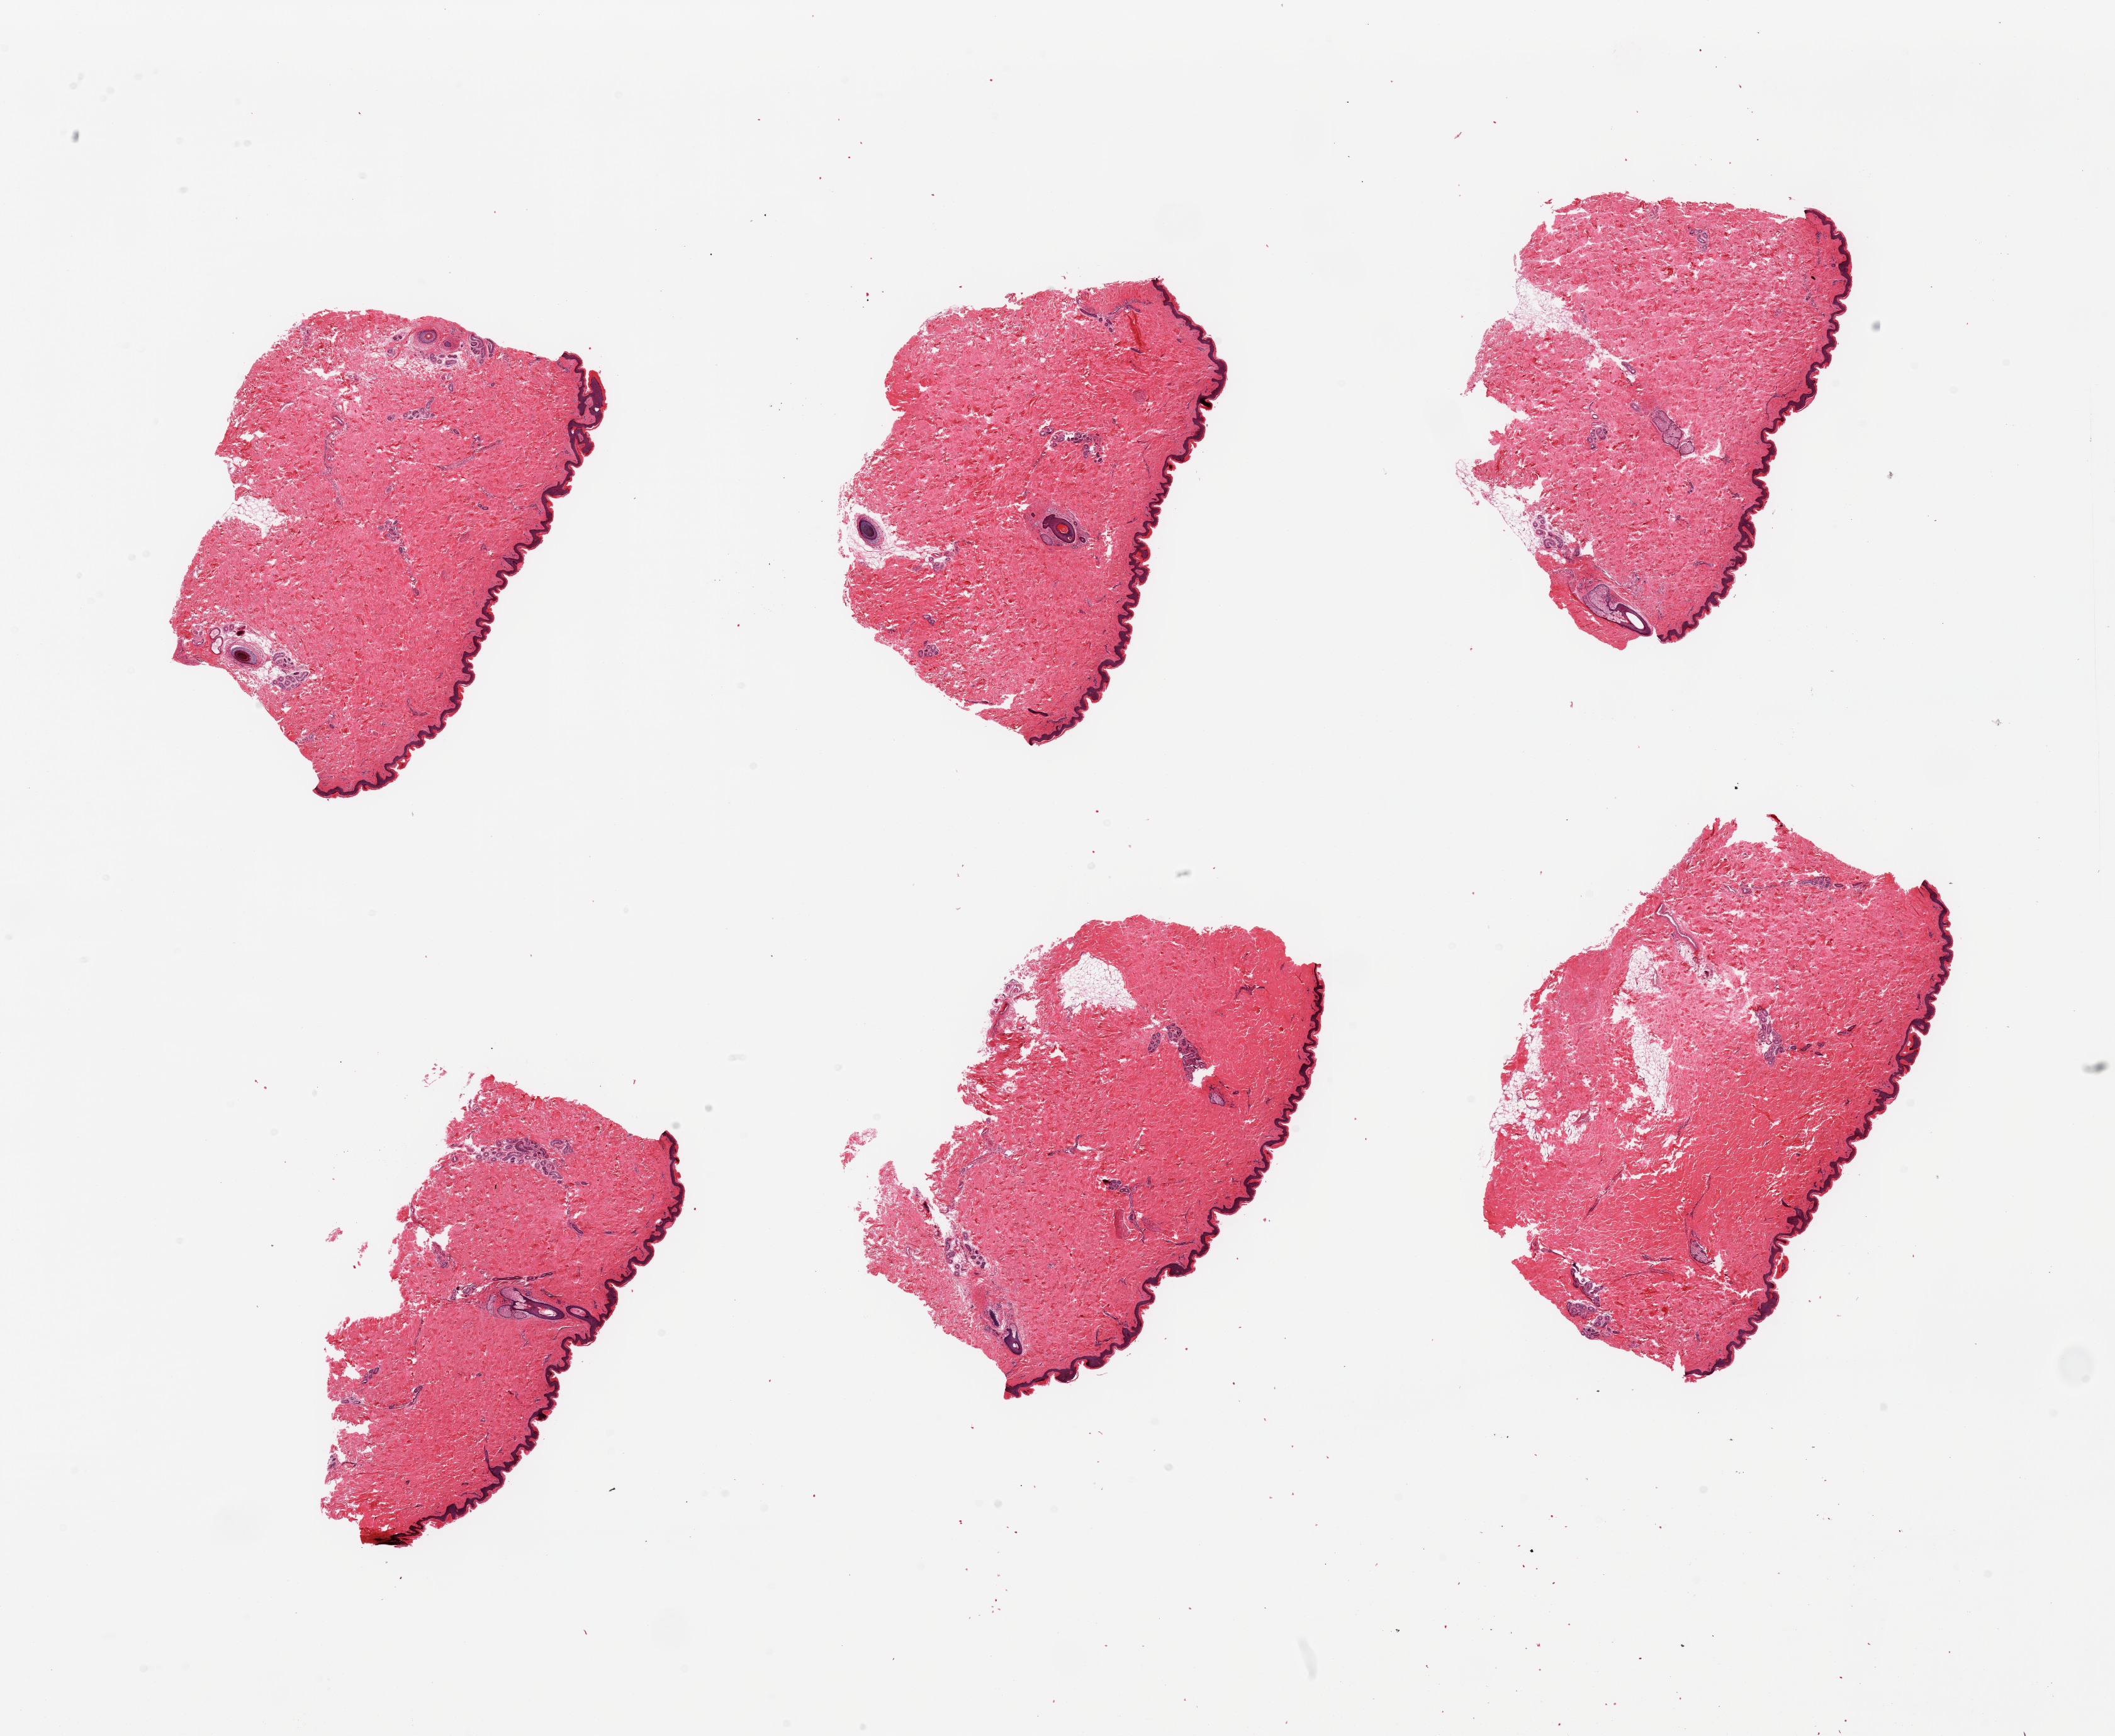
Whole-slide image, hematoxylin and eosin (H&E) stain — a low-resolution overview of the entire scanned area, about 26.6 x 21.8 mm (from a 20x scan); PAXgene-fixed, paraffin-embedded tissue; sampled site (target tissue): skin of suprapubic region; donor tissue sample. Donor sex: male.
Reviewer comment on this tissue sample: 6 pieces; well trimmed, <10% internal fat.